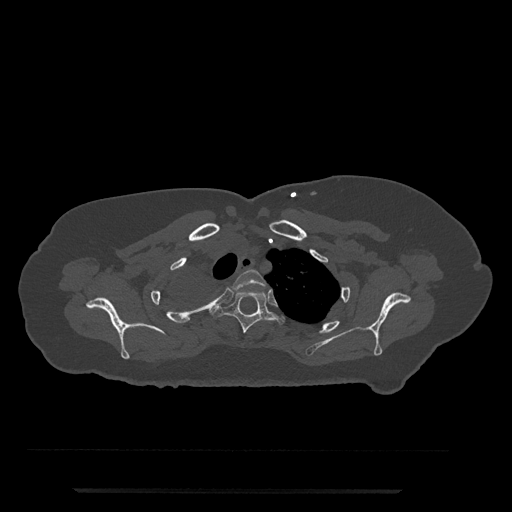
CT including the spine, one axial slice; slice 640 of 797 in the series (ordered by position); reconstruction kernel Br40s/3; 120 kVp; bone window (W 1800 / L 400 HU); 0.5 mm slice thickness; 512 × 512 image matrix, field of view 440 × 440 mm. Female patient, age 51 years. Case-level facts recorded for this patient, not image findings: primary cancer: neuro; vertebrae with lytic lesions (as recorded): T8.
Outlined on this slice (semi-automatically segmented with operator editing):
- T2 vertebra: box from (x=232, y=269) to (x=266, y=290) px
- T3 vertebra: (x=213, y=290)–(x=285, y=334)